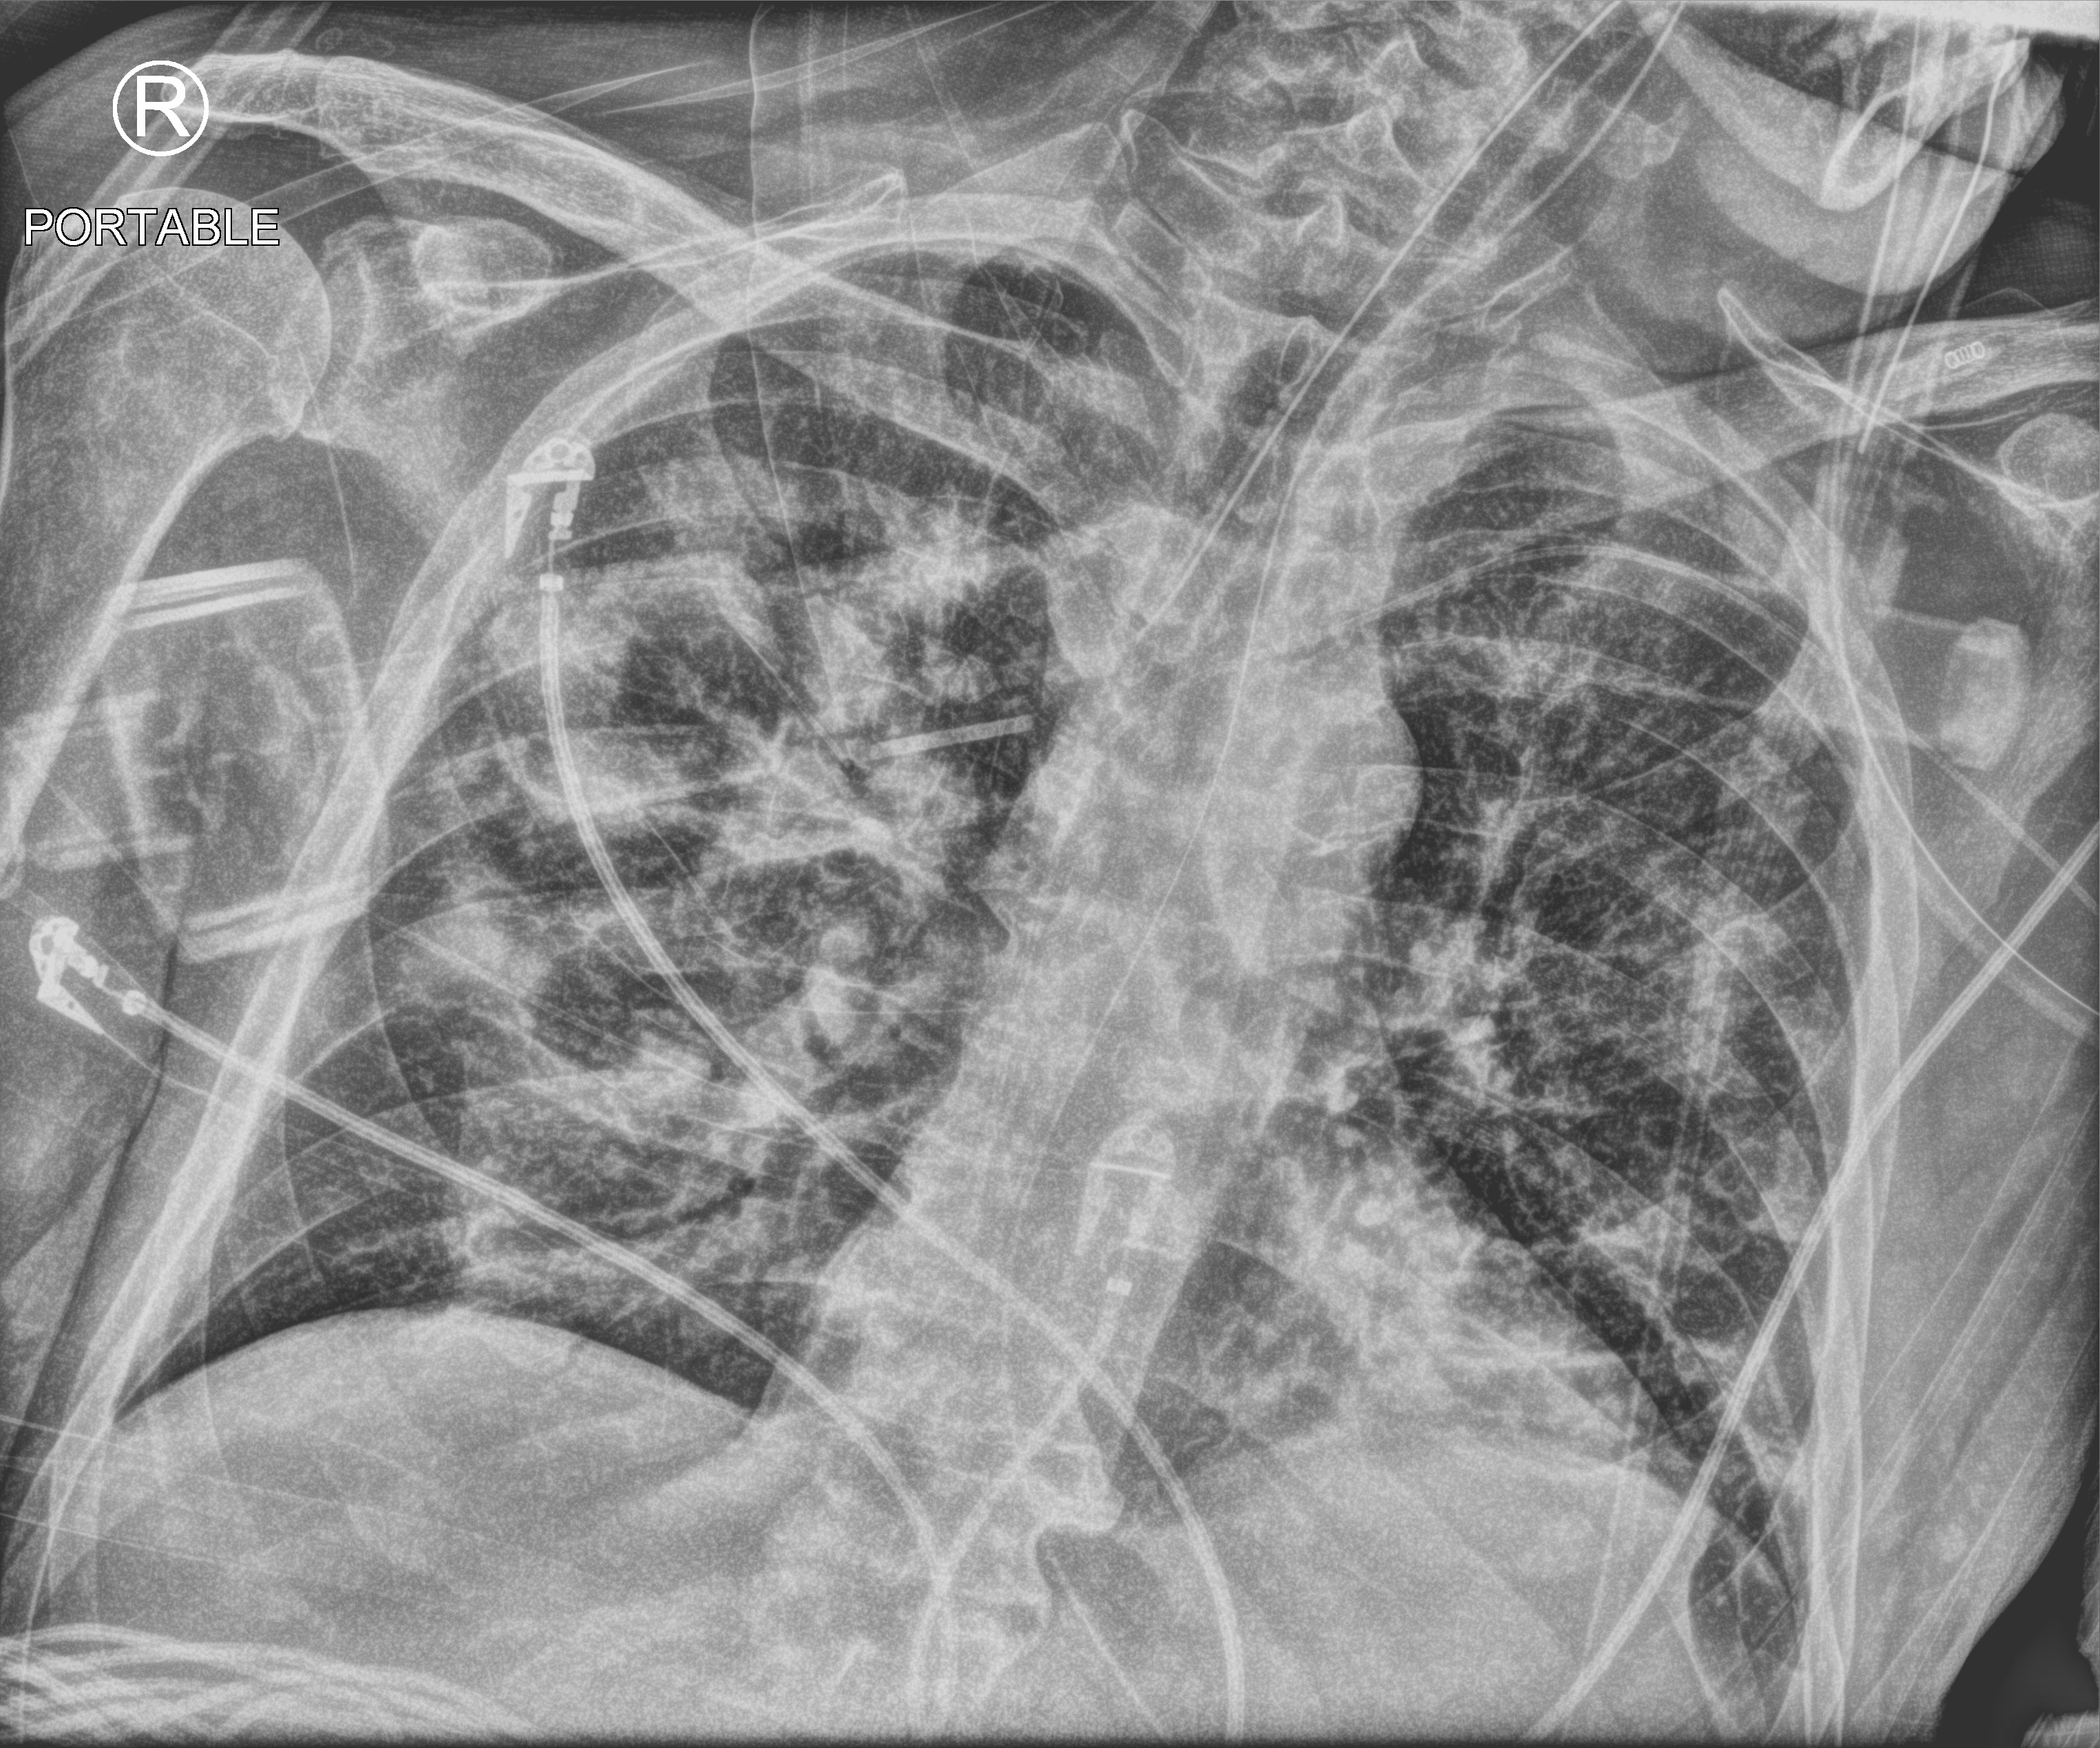
Bedside chest radiograph (computed radiography). Patient hospitalised with COVID-19; male, aged 60–74 years.
Admission-level facts for this patient (not findings on this image; timing relative to this image not recorded): mechanically ventilated during this hospital stay: yes.